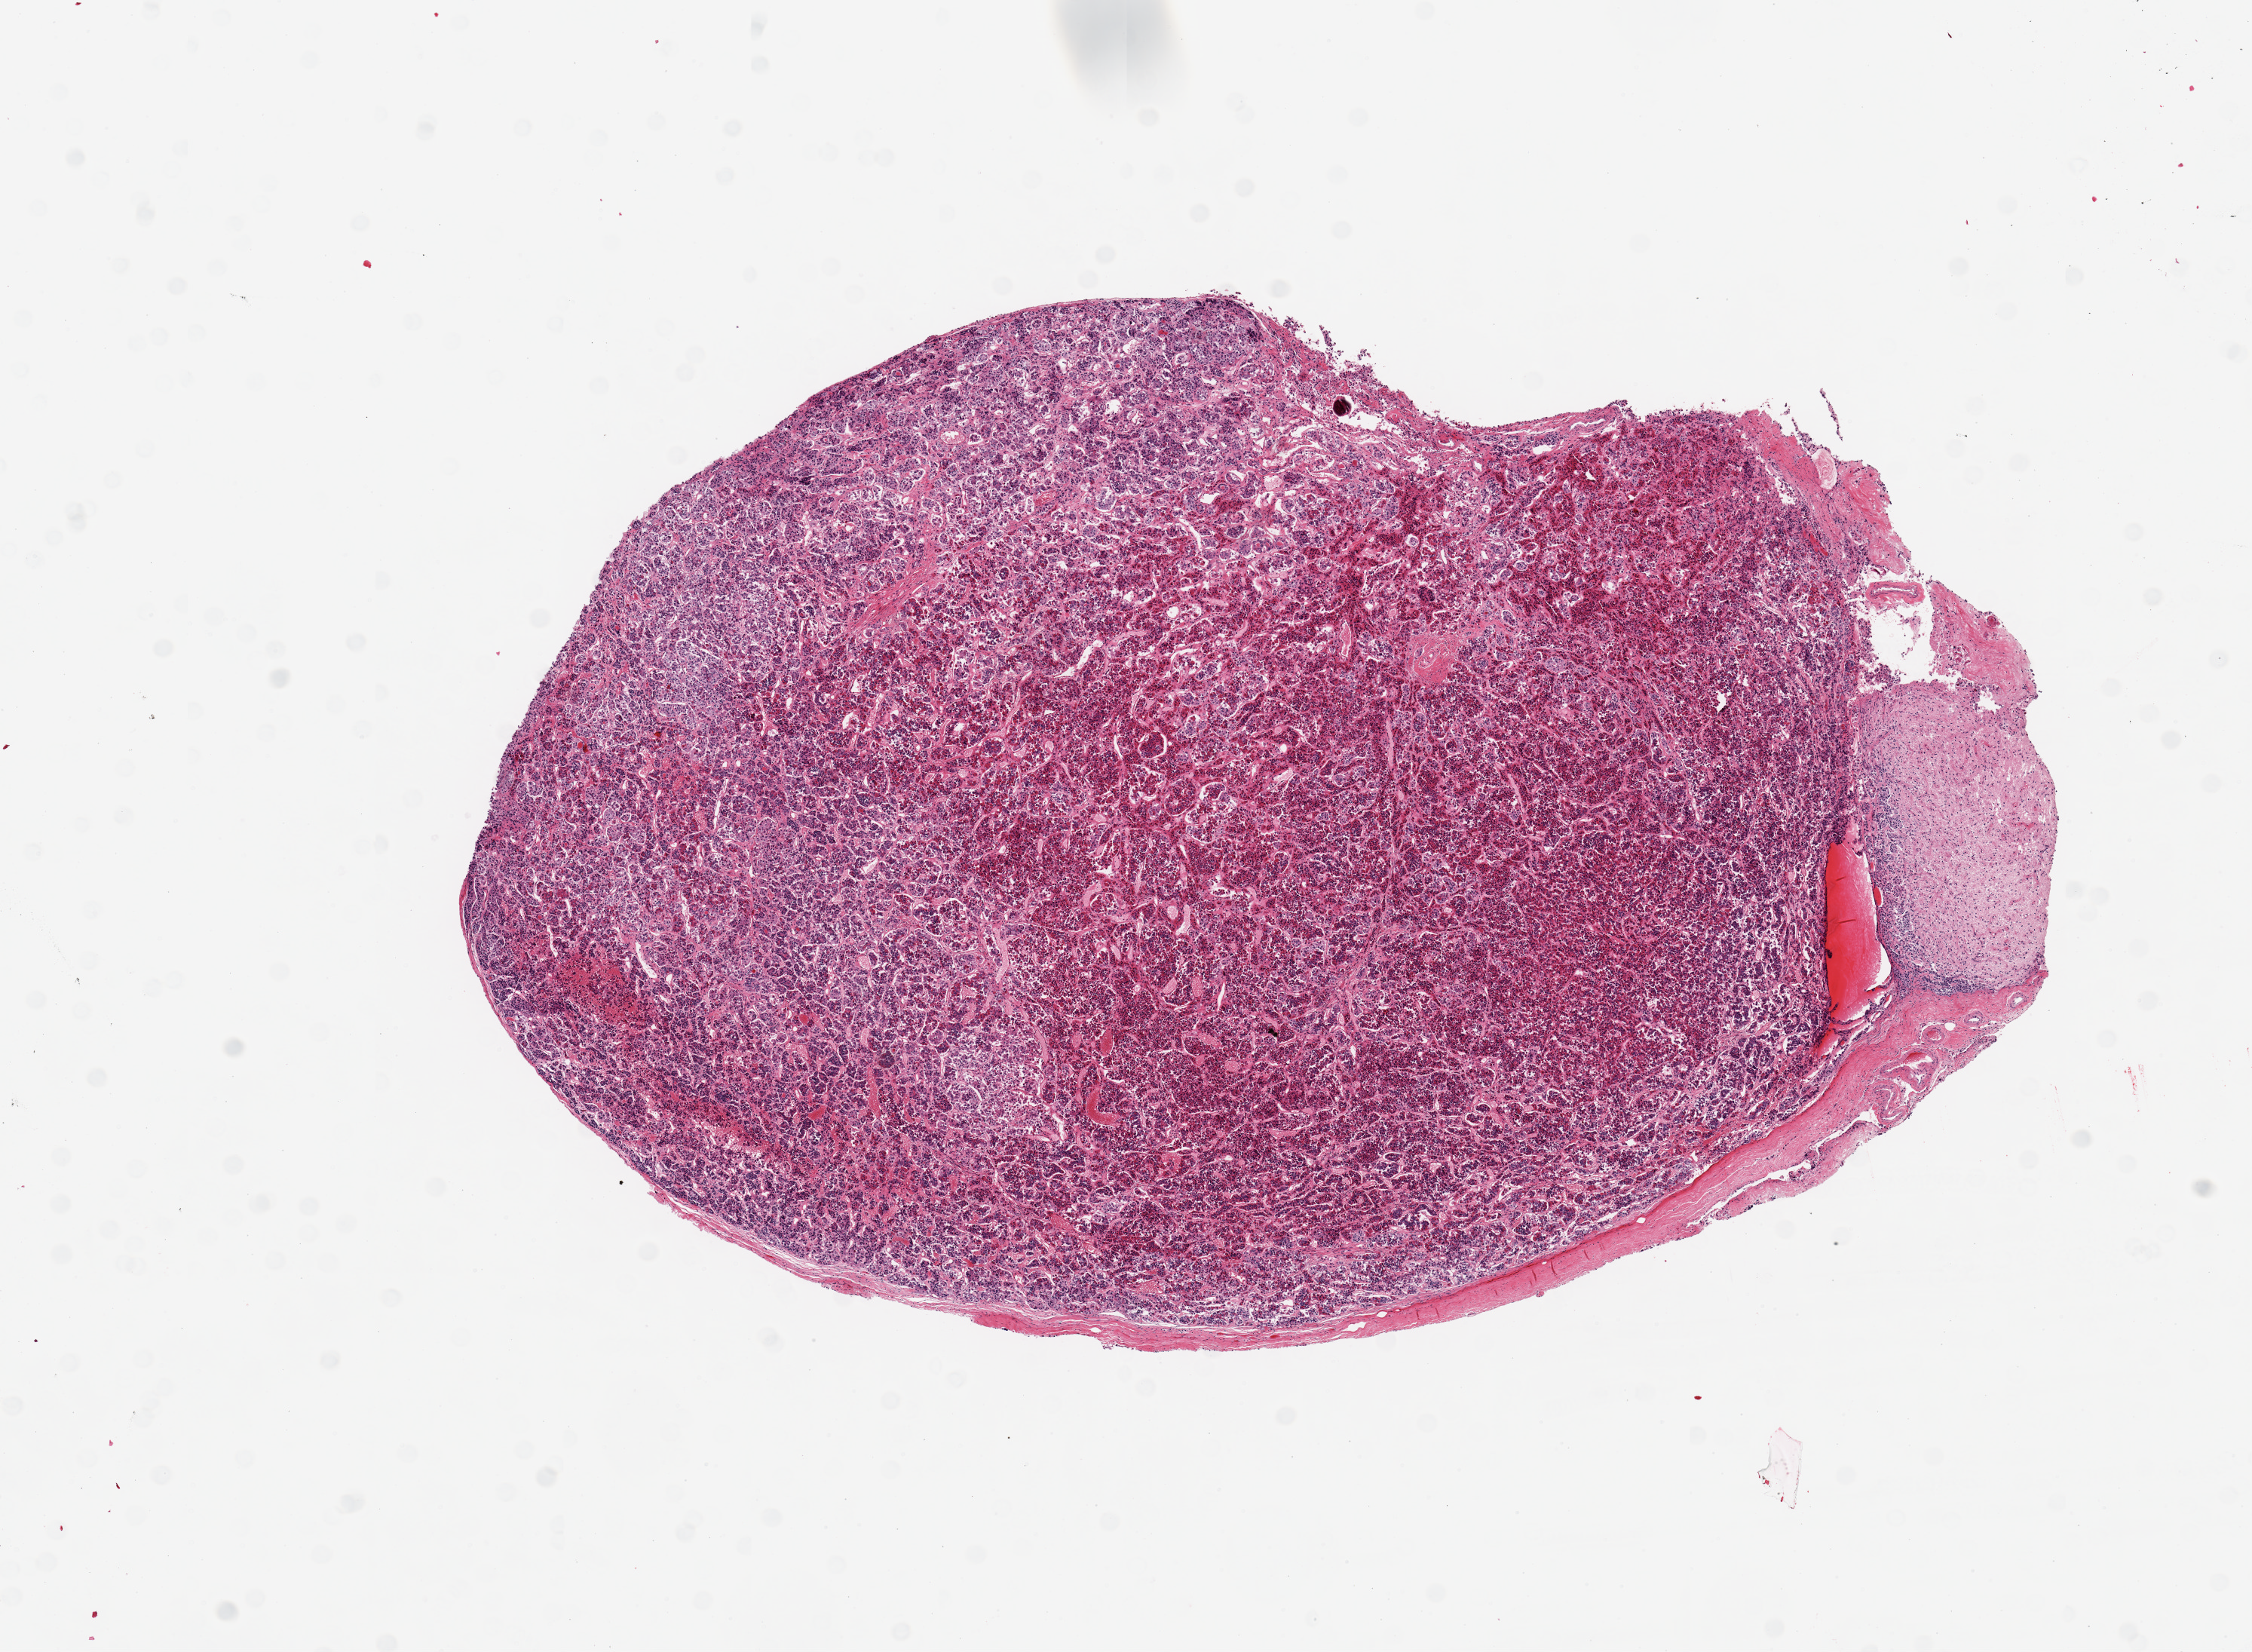
Digitized hematoxylin and eosin (H&E)-stained section, brightfield — whole scanned area (about 11.8 x 8.7 mm, from a 20x scan) shown as a low-resolution overview. PAXgene-fixed, paraffin-embedded tissue. Sampled site (target tissue): pituitary. Tissue donor sample. Donor sex: male.
Pathologist's review note for this sample: 1 piece, 8x5.5mm.